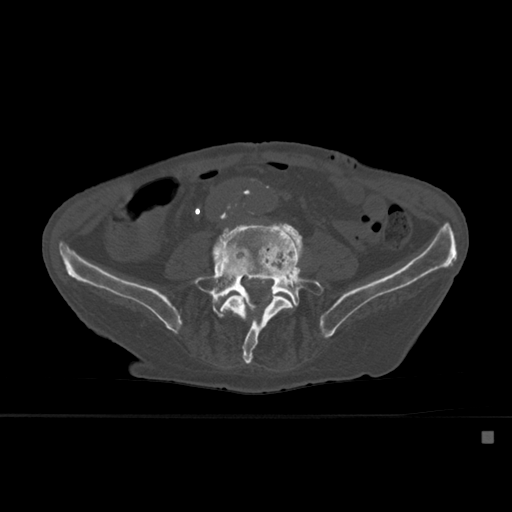
CT including the spine, one axial slice. Position 184 of 527 along the scan axis. Bone window (W 1800 / L 400 HU). 1.5 mm slice thickness. 512 × 512 image matrix, field of view 373 × 373 mm. Male patient, age 78 years. Case-level facts recorded for this patient, not image findings: primary cancer: prostate.
Annotated regions visible in this slice (semi-automatically segmented with operator editing):
- L4 vertebra: bounding box [x1, y1, x2, y2] px = [220, 272, 299, 365]
- L5 vertebra: [192, 227, 324, 318]